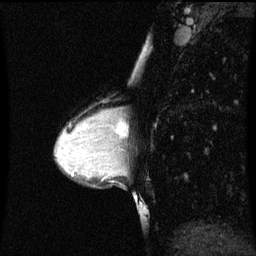
Breast MRI (dynamic contrast-enhanced), one sagittal slice; slice 34 of 60 in the series (ordered by position); dynamic contrast-enhanced series, image 2 of 3 at this slice position (ordered by acquisition); 1.5 T; TE 4.2 ms, TR 8.9 ms; 2 mm slice thickness; 256 × 256 image matrix, field of view 200 × 200 mm. Patient: female, 33 years. Case-level facts recorded for this patient, not image findings: setting: breast cancer imaged before/during neoadjuvant chemotherapy; receptor status: HER2-positive.
Annotated regions visible in this slice (semi-automatic segmentation, software-assisted and operator-edited):
- analysis volume of interest (the breast-tissue region the enhancement analysis was run in; not a lesion): bounding box <107,108,122,147> (left, top, right, bottom; pixels)
- tumour enhancement mask (voxels above the 70 % enhancement threshold inside the analysis volume of interest): <112,118,120,141>